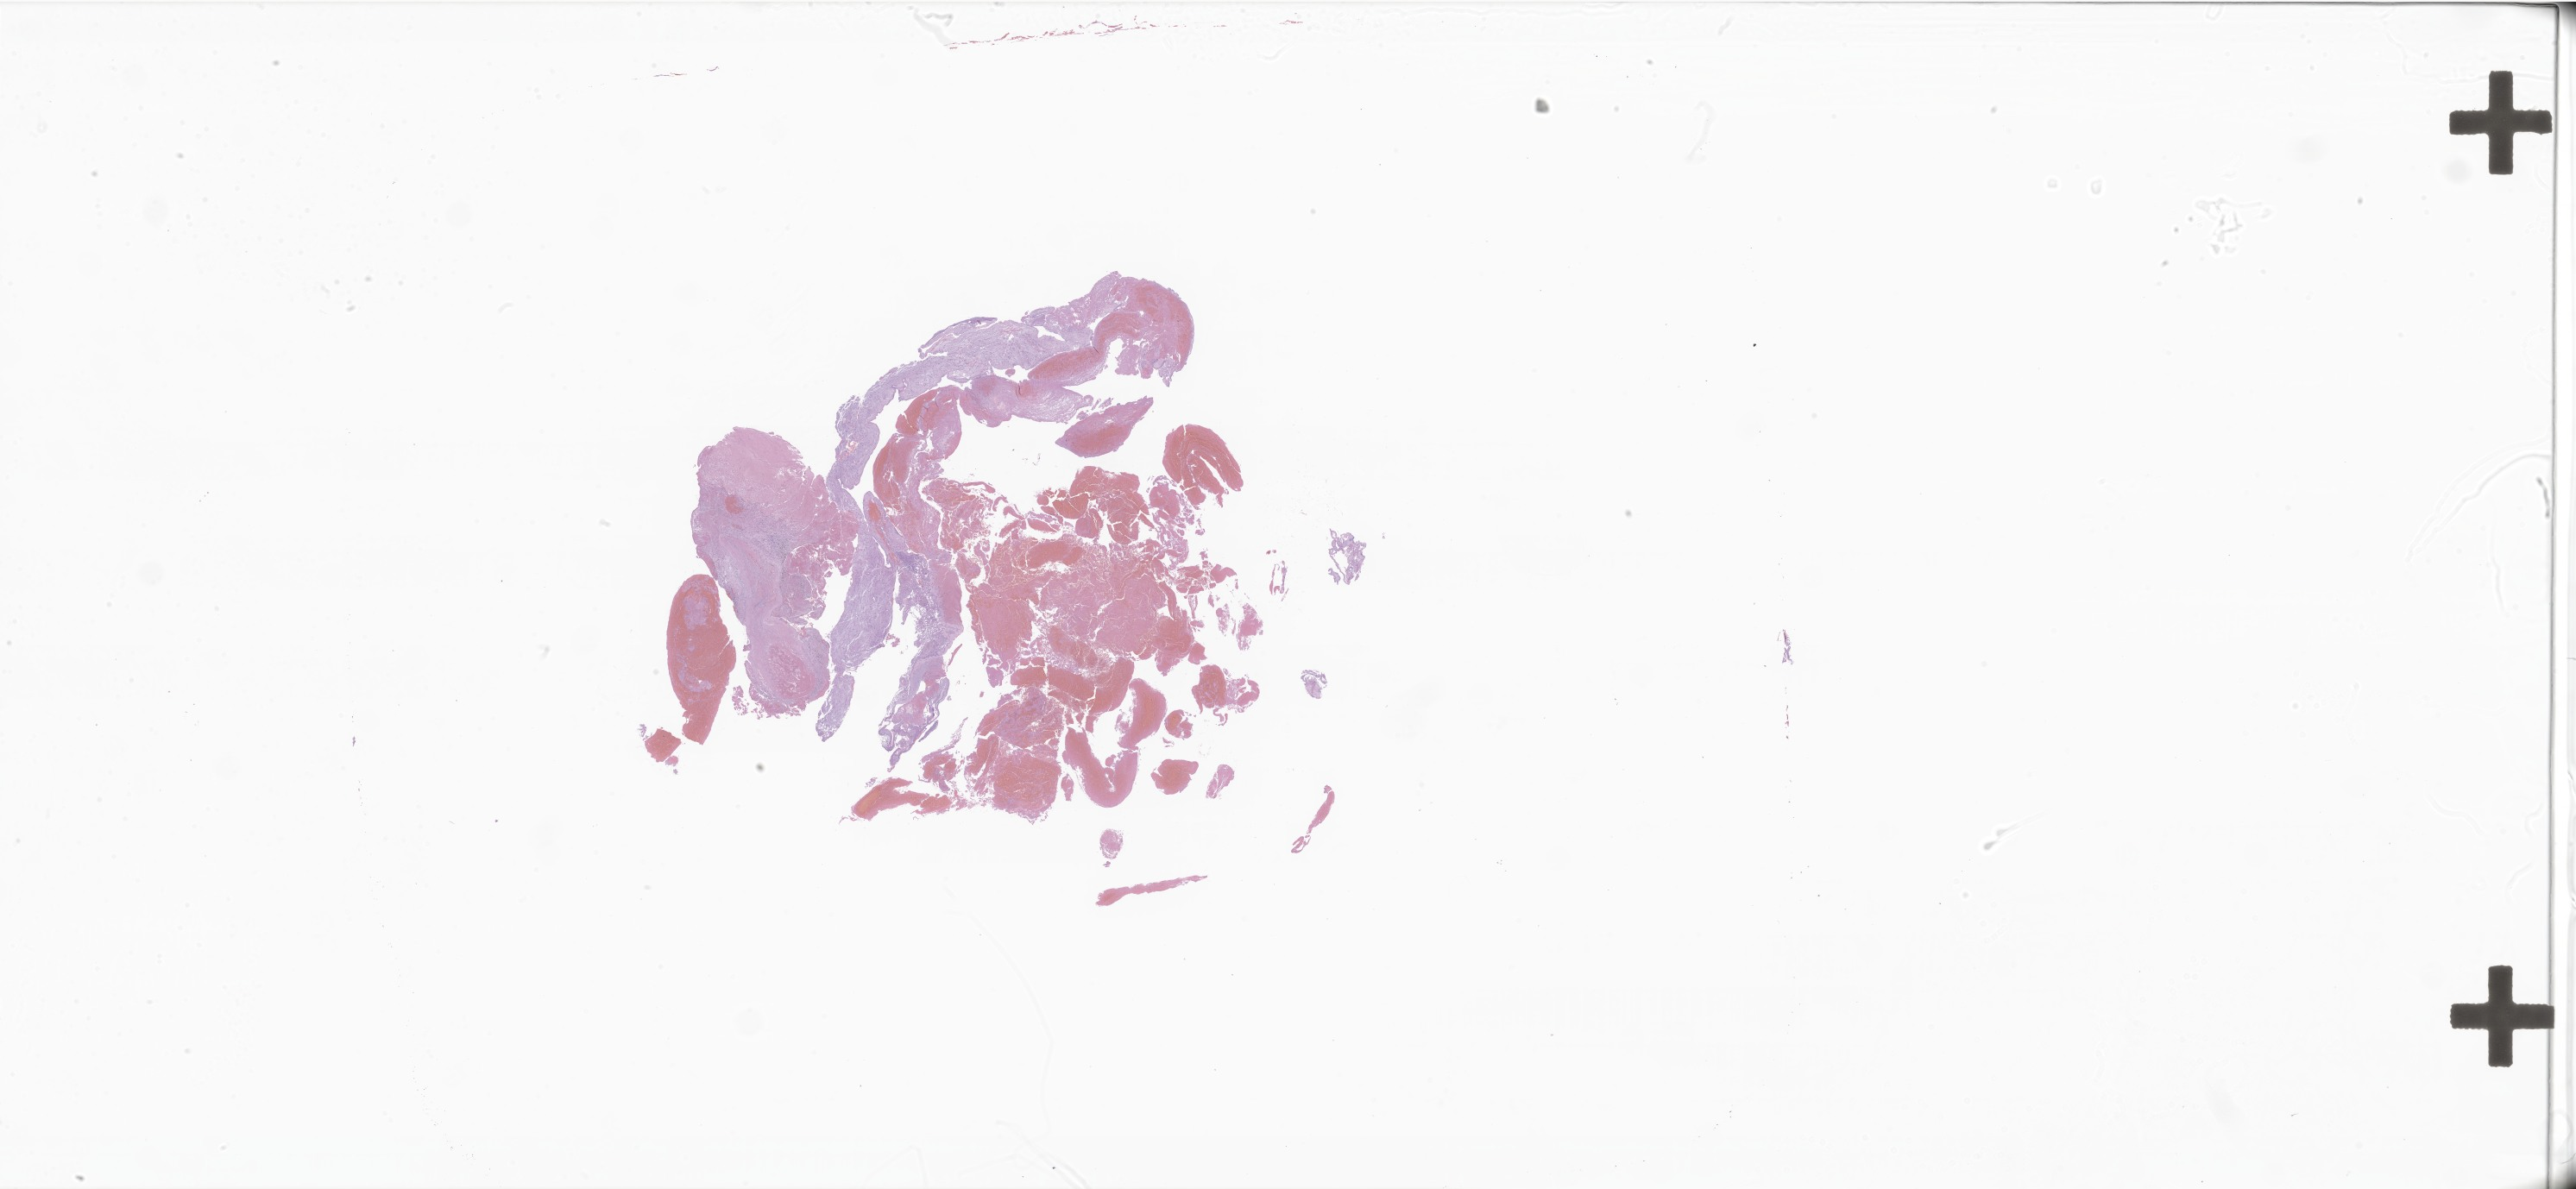
Digitized haematoxylin and eosin-stained section of tumor tissue from the brain — shown as a low-resolution overview of the whole scanned area (about 50.3 x 23.2 mm). Formalin-fixed paraffin-embedded section. Patient male; age 115 months (9 years 7 months).
Diagnosis (ICD-O-3 morphology term): Neoplasm, uncertain whether benign or malignant.